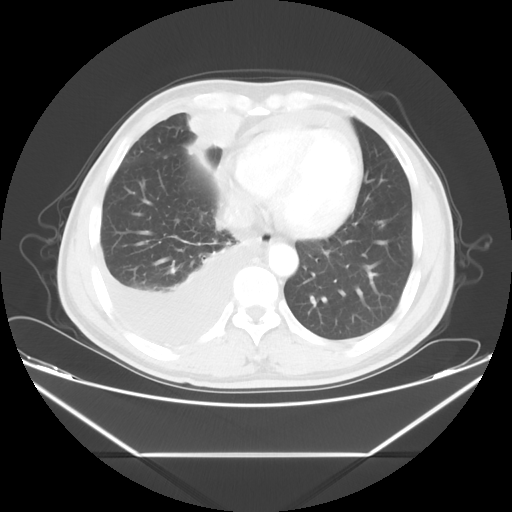
Chest CT, one axial slice; slice 16 of 56 in the series (ordered by position); reconstruction kernel STANDARD; 120 kVp; lung window (W 1500 / L -600 HU); 5 mm slice thickness; 512 × 512 image matrix. Patient: male, 57 years. Case-level facts recorded for this patient, not image findings: clinical TNM (as recorded): T2 N3 M1.
Structures marked on this image (bounding box drawn by a radiologist):
- lung tumour (recorded histology: adenocarcinoma): box from (x=184, y=112) to (x=246, y=153) px